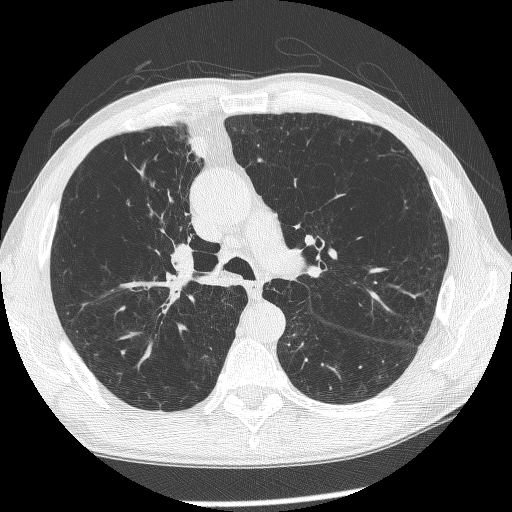
Low-dose screening chest CT, axial slice. Baseline annual screen. Lung window (W 1500 / L -600 HU). 1.25 mm slice thickness. Male, age 60 years at enrolment.
- Expert reader's lesion annotation, box from (x=144, y=211) to (x=227, y=303) px.
- Screening reader's record for this exam (one nodule recorded; not confirmed to be the boxed lesion): non-calcified nodule or mass ≥4 mm, right upper lobe, 12 × 8 mm, spiculated (stellate) margins, mixed attenuation.
- Participant outcome: lung cancer diagnosed 208 days after this screen — squamous cell carcinoma, NOS, right upper lobe, right middle lobe, right main stem bronchus, poorly differentiated (G3), stage IV (AJCC 6th edition).